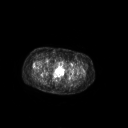
FDG PET of an extremity soft-tissue mass (from a PET/CT study), one axial slice. Slice 63 of 267 in the series (ordered by position). 128 × 128 image matrix. Patient: female, 70 years. Case-level facts recorded for this patient, not image findings: histological type: synovial sarcoma; grade: intermediate; site of the primary tumour: right buttock.
Annotated regions visible in this slice (expert contour drawn on MRI and transferred to this co-registered scan by the dataset authors):
- gross tumour volume including surrounding oedema: bounding box <36,74,43,79> (left, top, right, bottom; pixels)